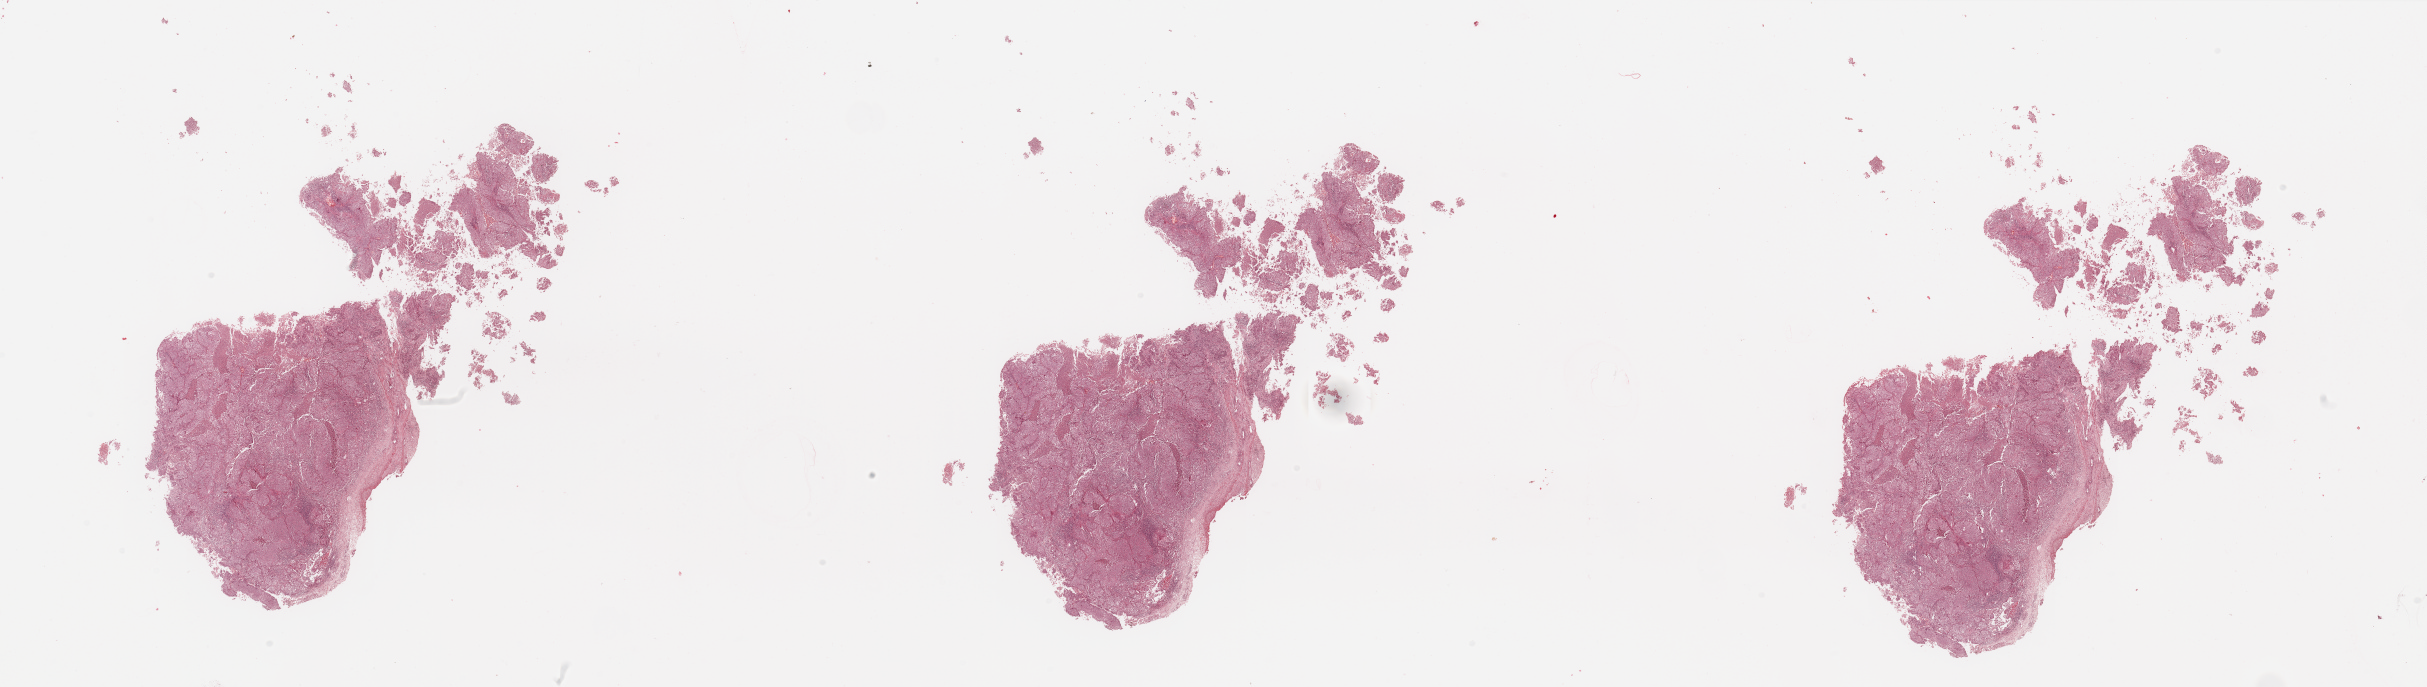
Whole-slide histology image, H&E-stained, a low-resolution overview of the entire scanned area, about 38.4 x 10.9 mm, lung, tumour tissue. Patient: male, age 71 years.
Patient diagnosis (cohort enrolment): squamous cell carcinoma (lung).